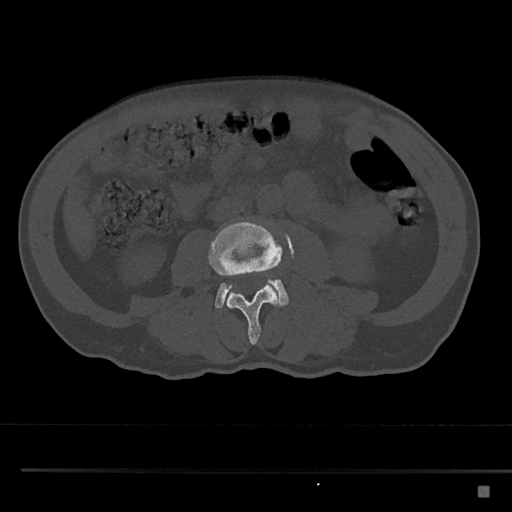
CT including the spine, one axial slice; position 674 of 797 along the scan axis; reconstruction kernel Br40s/3; bone window (W 1800 / L 400 HU); 0.5 mm slice thickness; 512 × 512 image matrix. Patient: male, 59 years. From the clinical record (not read from this slice): primary cancer: prostate.
Outlined on this slice (semi-automatically segmented with operator editing):
- L3 vertebra: bounding box [x1, y1, x2, y2] px = [208, 220, 283, 345]
- L4 vertebra: [215, 278, 289, 309]